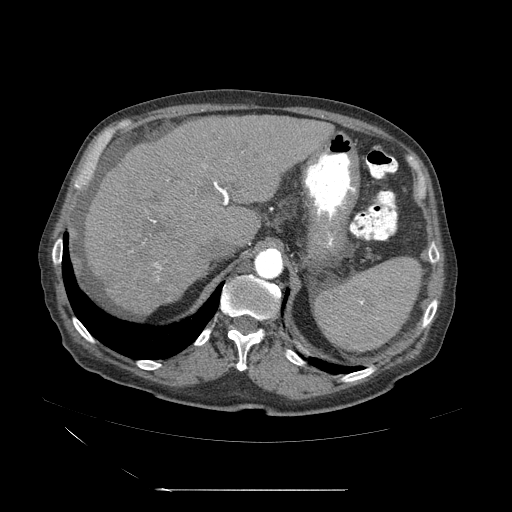
Contrast-enhanced abdominal CT (liver protocol), one axial slice; slice 35 of 71 in the series (ordered by position); reconstruction kernel STANDARD; soft-tissue window (W 400 / L 40 HU); 512 × 512 image matrix, field of view 440 × 440 mm. From the clinical record (not read from this slice): diagnosis: hepatocellular carcinoma (patient treated with transarterial chemoembolisation; whether this scan precedes or follows treatment is not stated here); TNM stage (as recorded): Stage-II; Child-Pugh class: A; tumour size: 1 cm.
Annotated regions visible in this slice (semi-automatic segmentation, software-assisted and operator-edited):
- abdominal aorta: box from (x=254, y=249) to (x=283, y=279) px
- liver parenchyma outside the tumour (the mass and vessels are separate outlines, so this box may not span the whole liver): (x=77, y=116)–(x=333, y=322)
- liver vessels: (x=134, y=161)–(x=235, y=291)